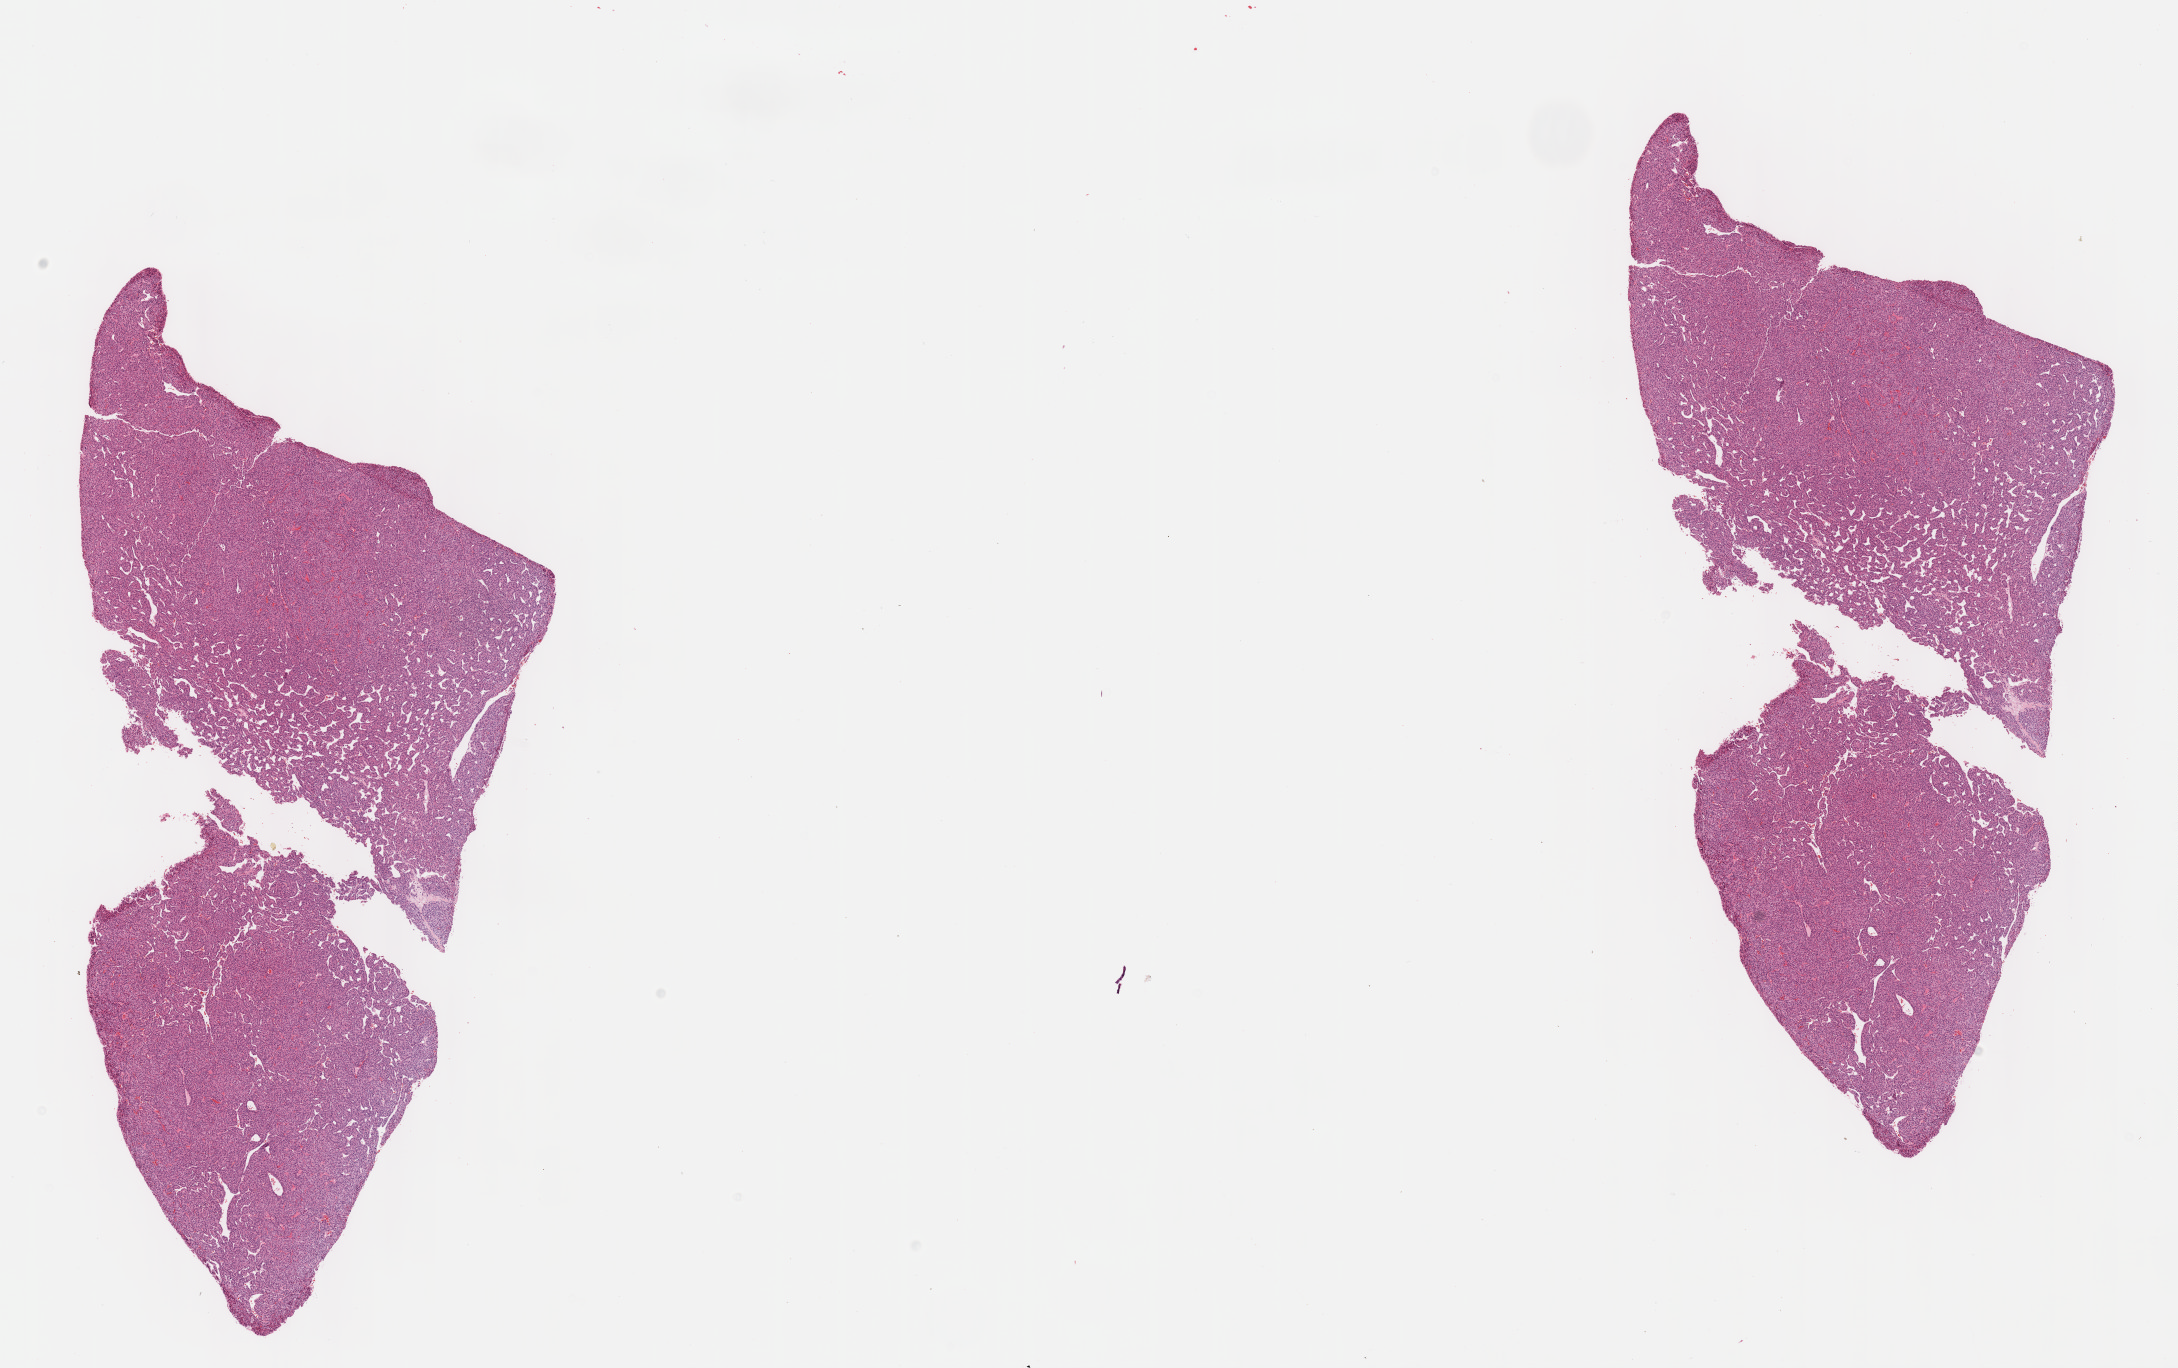
Whole-slide histology image, H&E — whole scanned area (about 17.6 x 11.1 mm) shown as a low-resolution overview. Formalin-fixed paraffin-embedded (FFPE) diagnostic section. Liver, primary tumour sample. Patient: male, age at initial diagnosis 39 years. Histologic grade: G3 (poorly differentiated).
Histologic diagnosis: Hepatocellular carcinoma, NOS. AJCC pathologic stage: I (6th edition).